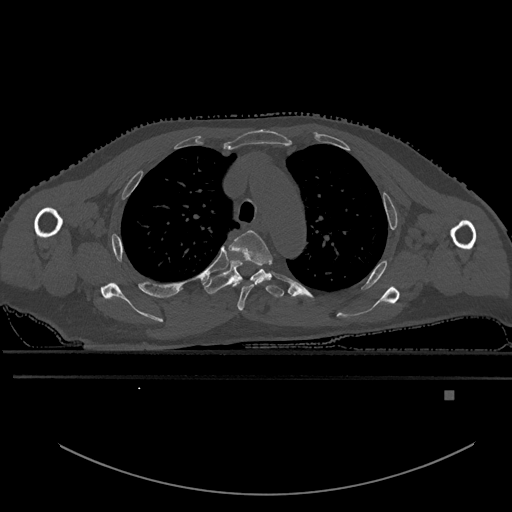
CT including the spine, one axial slice. Slice 427 of 969 in the series (ordered by position). Bone window (W 1800 / L 400 HU). 0.5 mm slice thickness. 512 × 512 image matrix, field of view 456 × 456 mm. Patient: male, 82 years. Case-level facts recorded for this patient, not image findings: primary cancer: prostate; vertebrae with lytic lesions (as recorded): T11, T9, T8, T2.
Outlined on this slice (semi-automatic segmentation, software-assisted and operator-edited):
- T3 vertebra: bounding box [x1, y1, x2, y2] px = [229, 230, 273, 311]
- T4 vertebra: [203, 261, 284, 298]